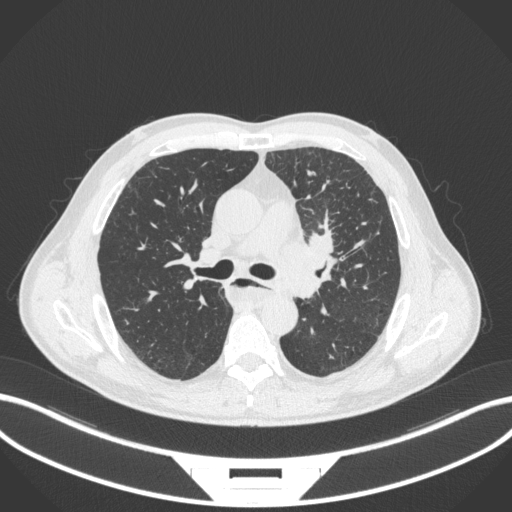
Chest CT, one axial slice. Reconstruction kernel B31f. Lung window (W 1500 / L -600 HU). 1 mm slice thickness. 512 × 512 image matrix, field of view 400 × 400 mm. Patient: male, 57 years. Case-level facts recorded for this patient, not image findings: clinical TNM (as recorded): T2a N1 M0.
Structures marked on this image (rectangle marked by the reading radiologist):
- lung tumour (recorded histology: squamous cell carcinoma): bounding box (x1, y1, x2, y2) in pixels: (277, 225, 346, 283)